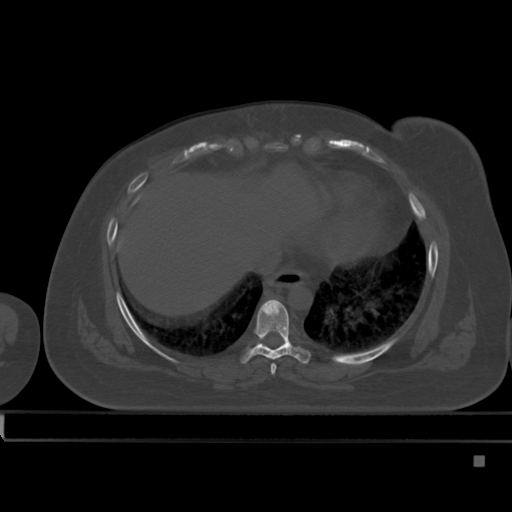
CT including the spine, one axial slice; slice 277 of 495 in the series (ordered by position); bone window (W 1800 / L 400 HU); 1.5 mm slice thickness; 512 × 512 image matrix, field of view 404 × 404 mm. Patient: female, 33 years. From the clinical record (not read from this slice): primary cancer: breast.
Annotated regions visible in this slice (semi-automatic segmentation, software-assisted and operator-edited):
- T7 vertebra: bounding box (x1, y1, x2, y2) in pixels: (271, 364, 277, 375)
- T8 vertebra: (240, 299, 310, 364)